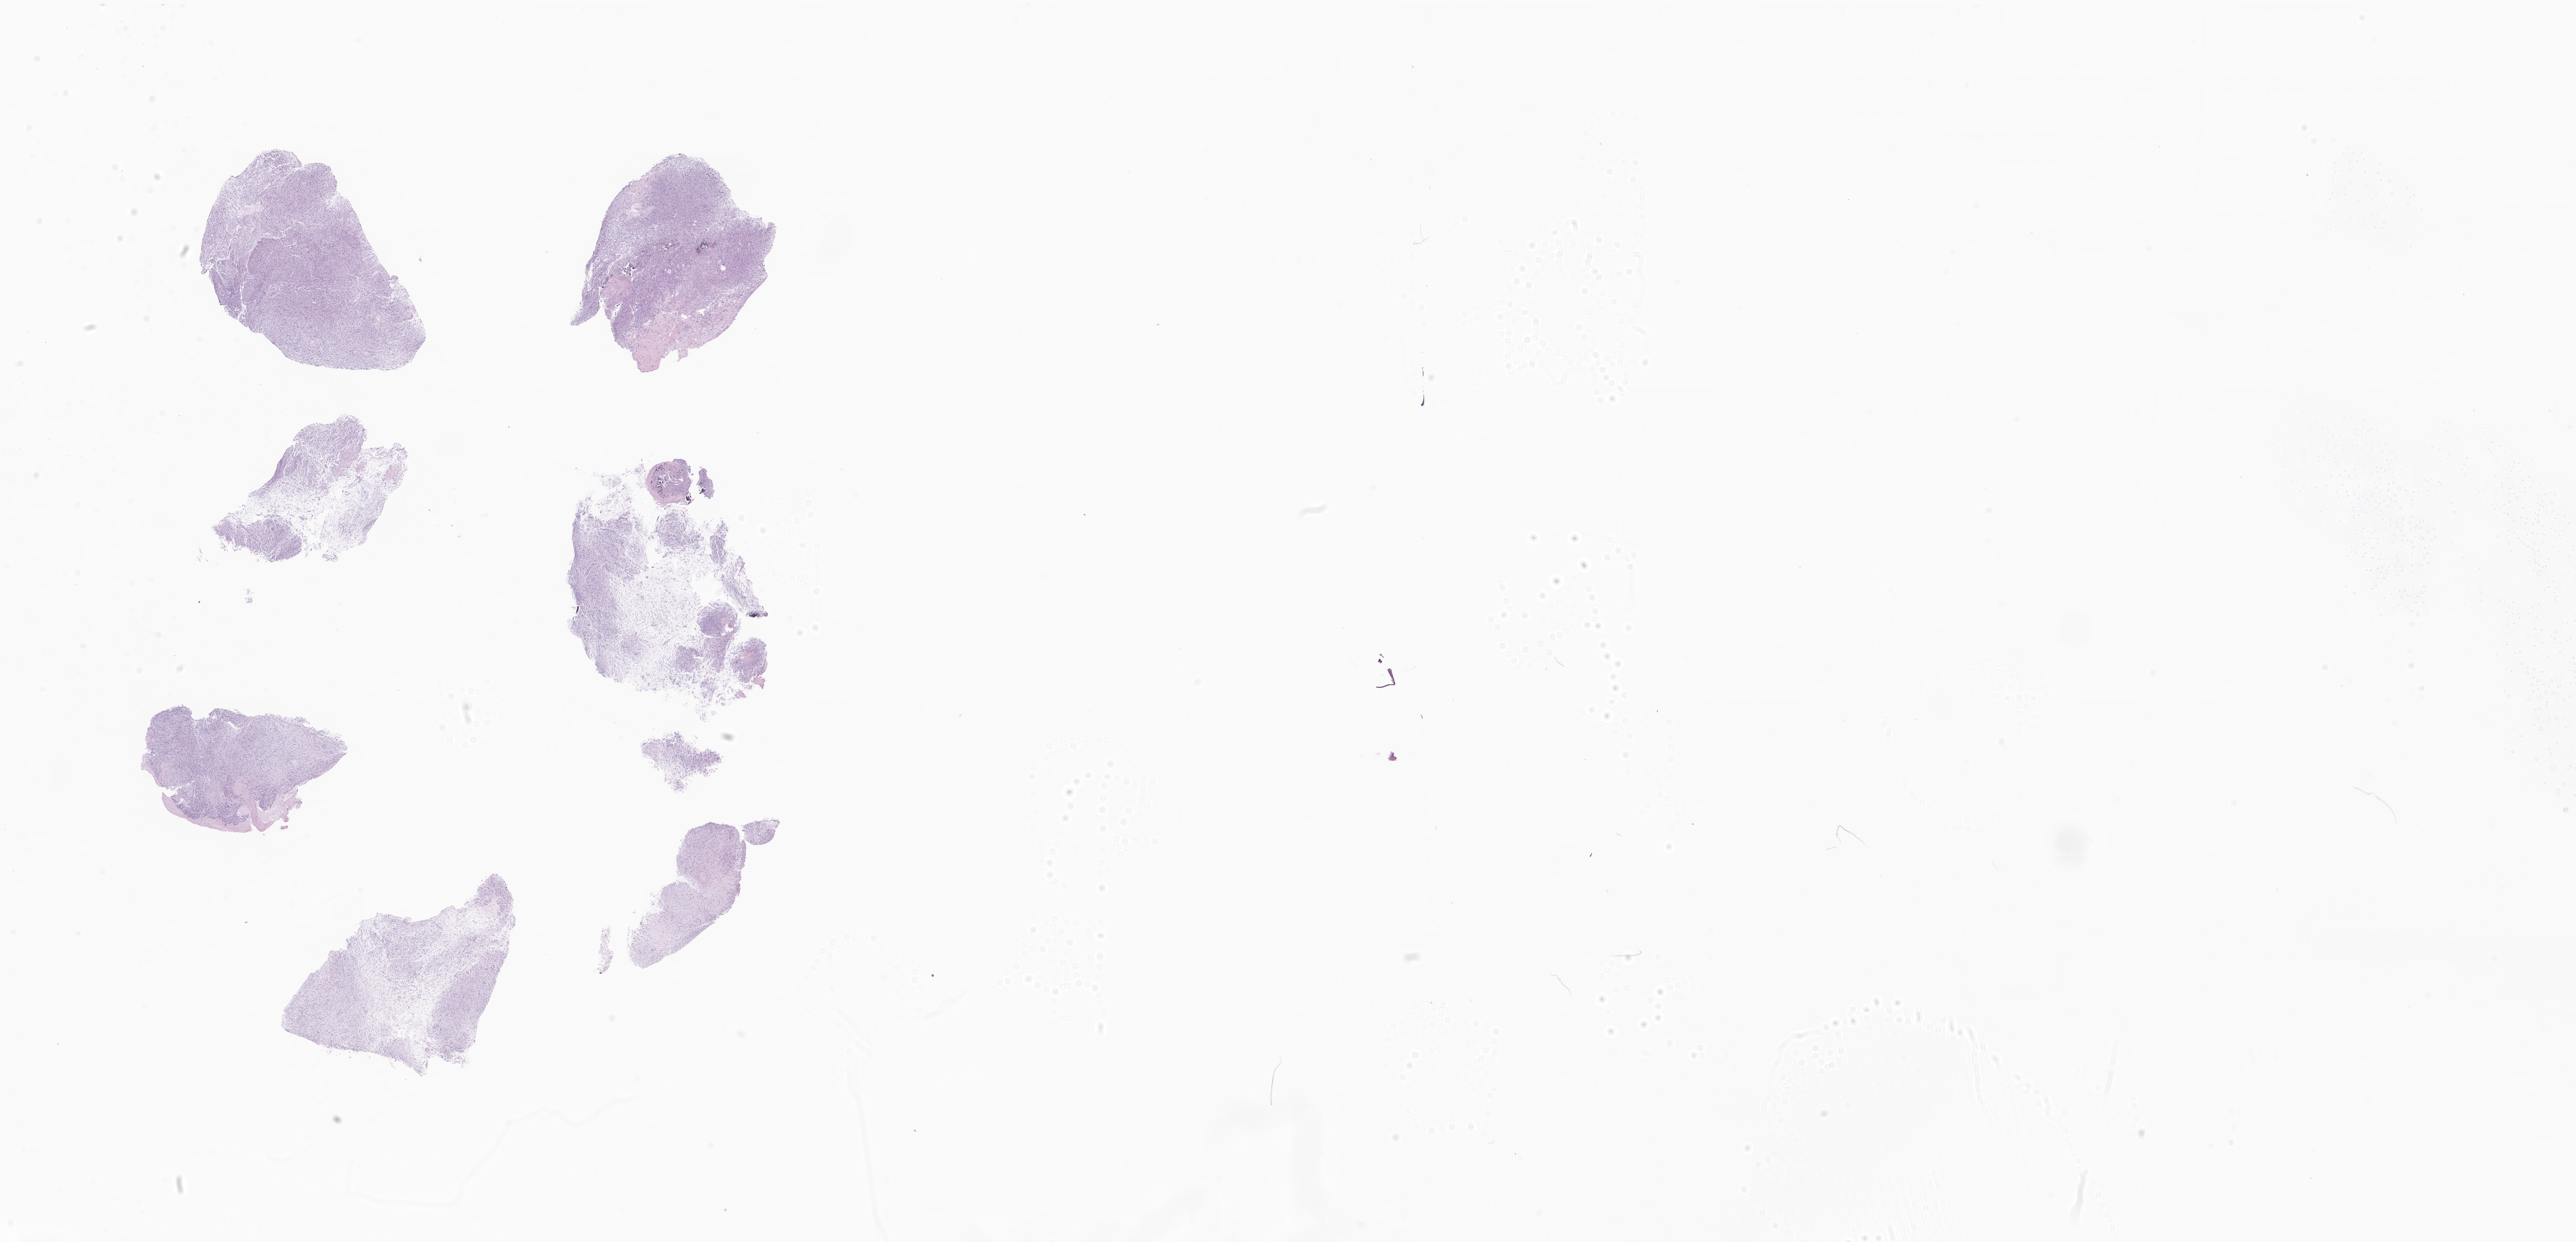
Whole-slide image, haematoxylin and eosin stain of tumor tissue from the brain — low-resolution overview of the scanned area, about 35.3 x 17.0 mm. FFPE section. Patient male; age 107 months (8 years 11 months).
Diagnosis: Neoplasm, benign.